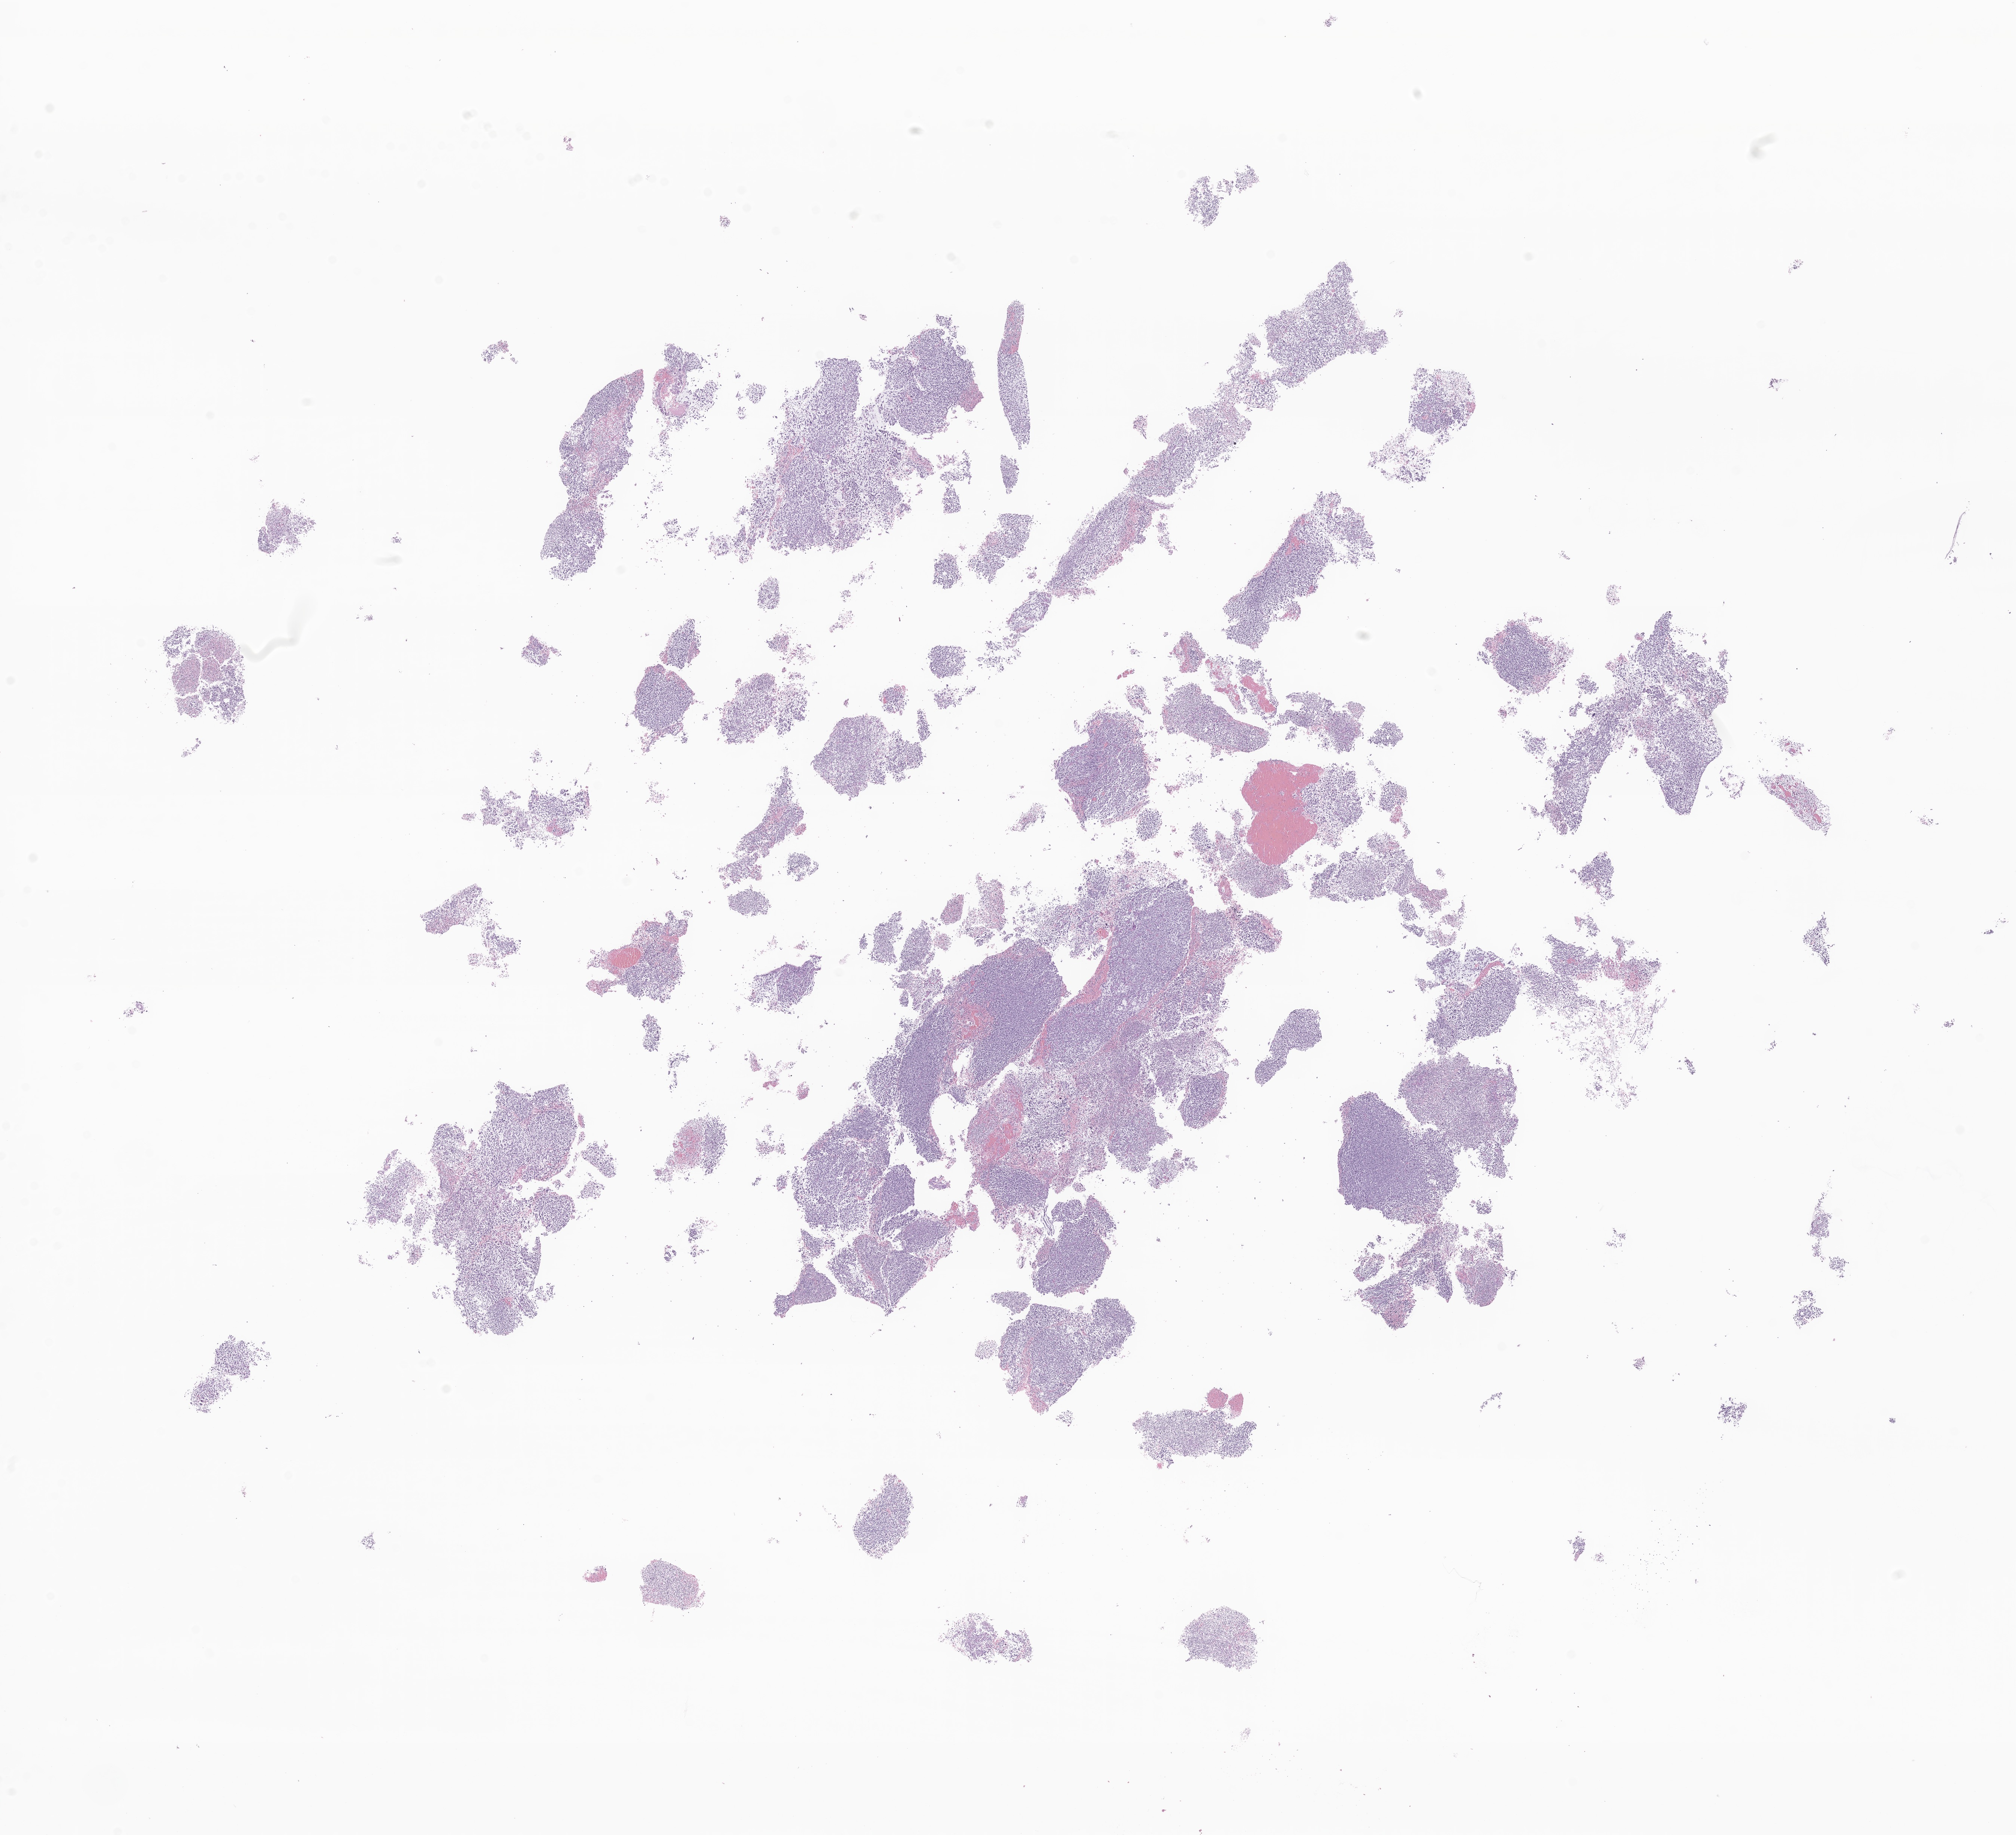
Whole-slide image, hematoxylin and eosin (H&E) stain of tumor tissue from the brain — low-resolution overview of the scanned area, about 22.7 x 20.7 mm; FFPE section. Patient: male, age 153 months (12 years 9 months).
Diagnosis (ICD-O-3 morphology term): Astrocytoma, NOS.